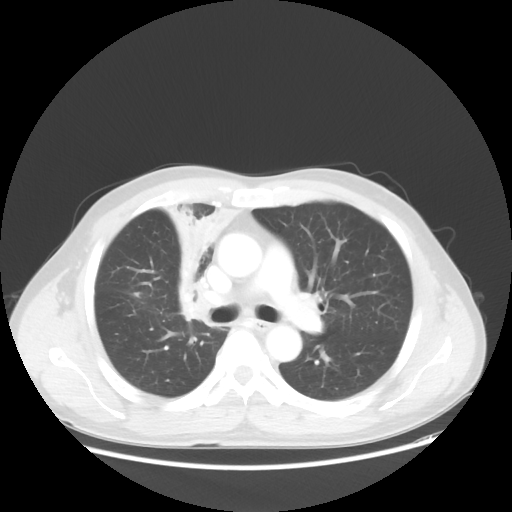
Chest CT, one axial slice; position 34 of 56 along the scan axis; reconstruction kernel STANDARD; lung window (W 1500 / L -600 HU); 5 mm slice thickness; 512 × 512 image matrix. Patient: male, 60 years. From the clinical record (not read from this slice): clinical TNM (as recorded): T2a N1 M0.
Outlined on this slice (rectangle marked by the reading radiologist):
- lung tumour (recorded histology: squamous cell carcinoma): bounding box [x1, y1, x2, y2] px = [148, 171, 237, 338]